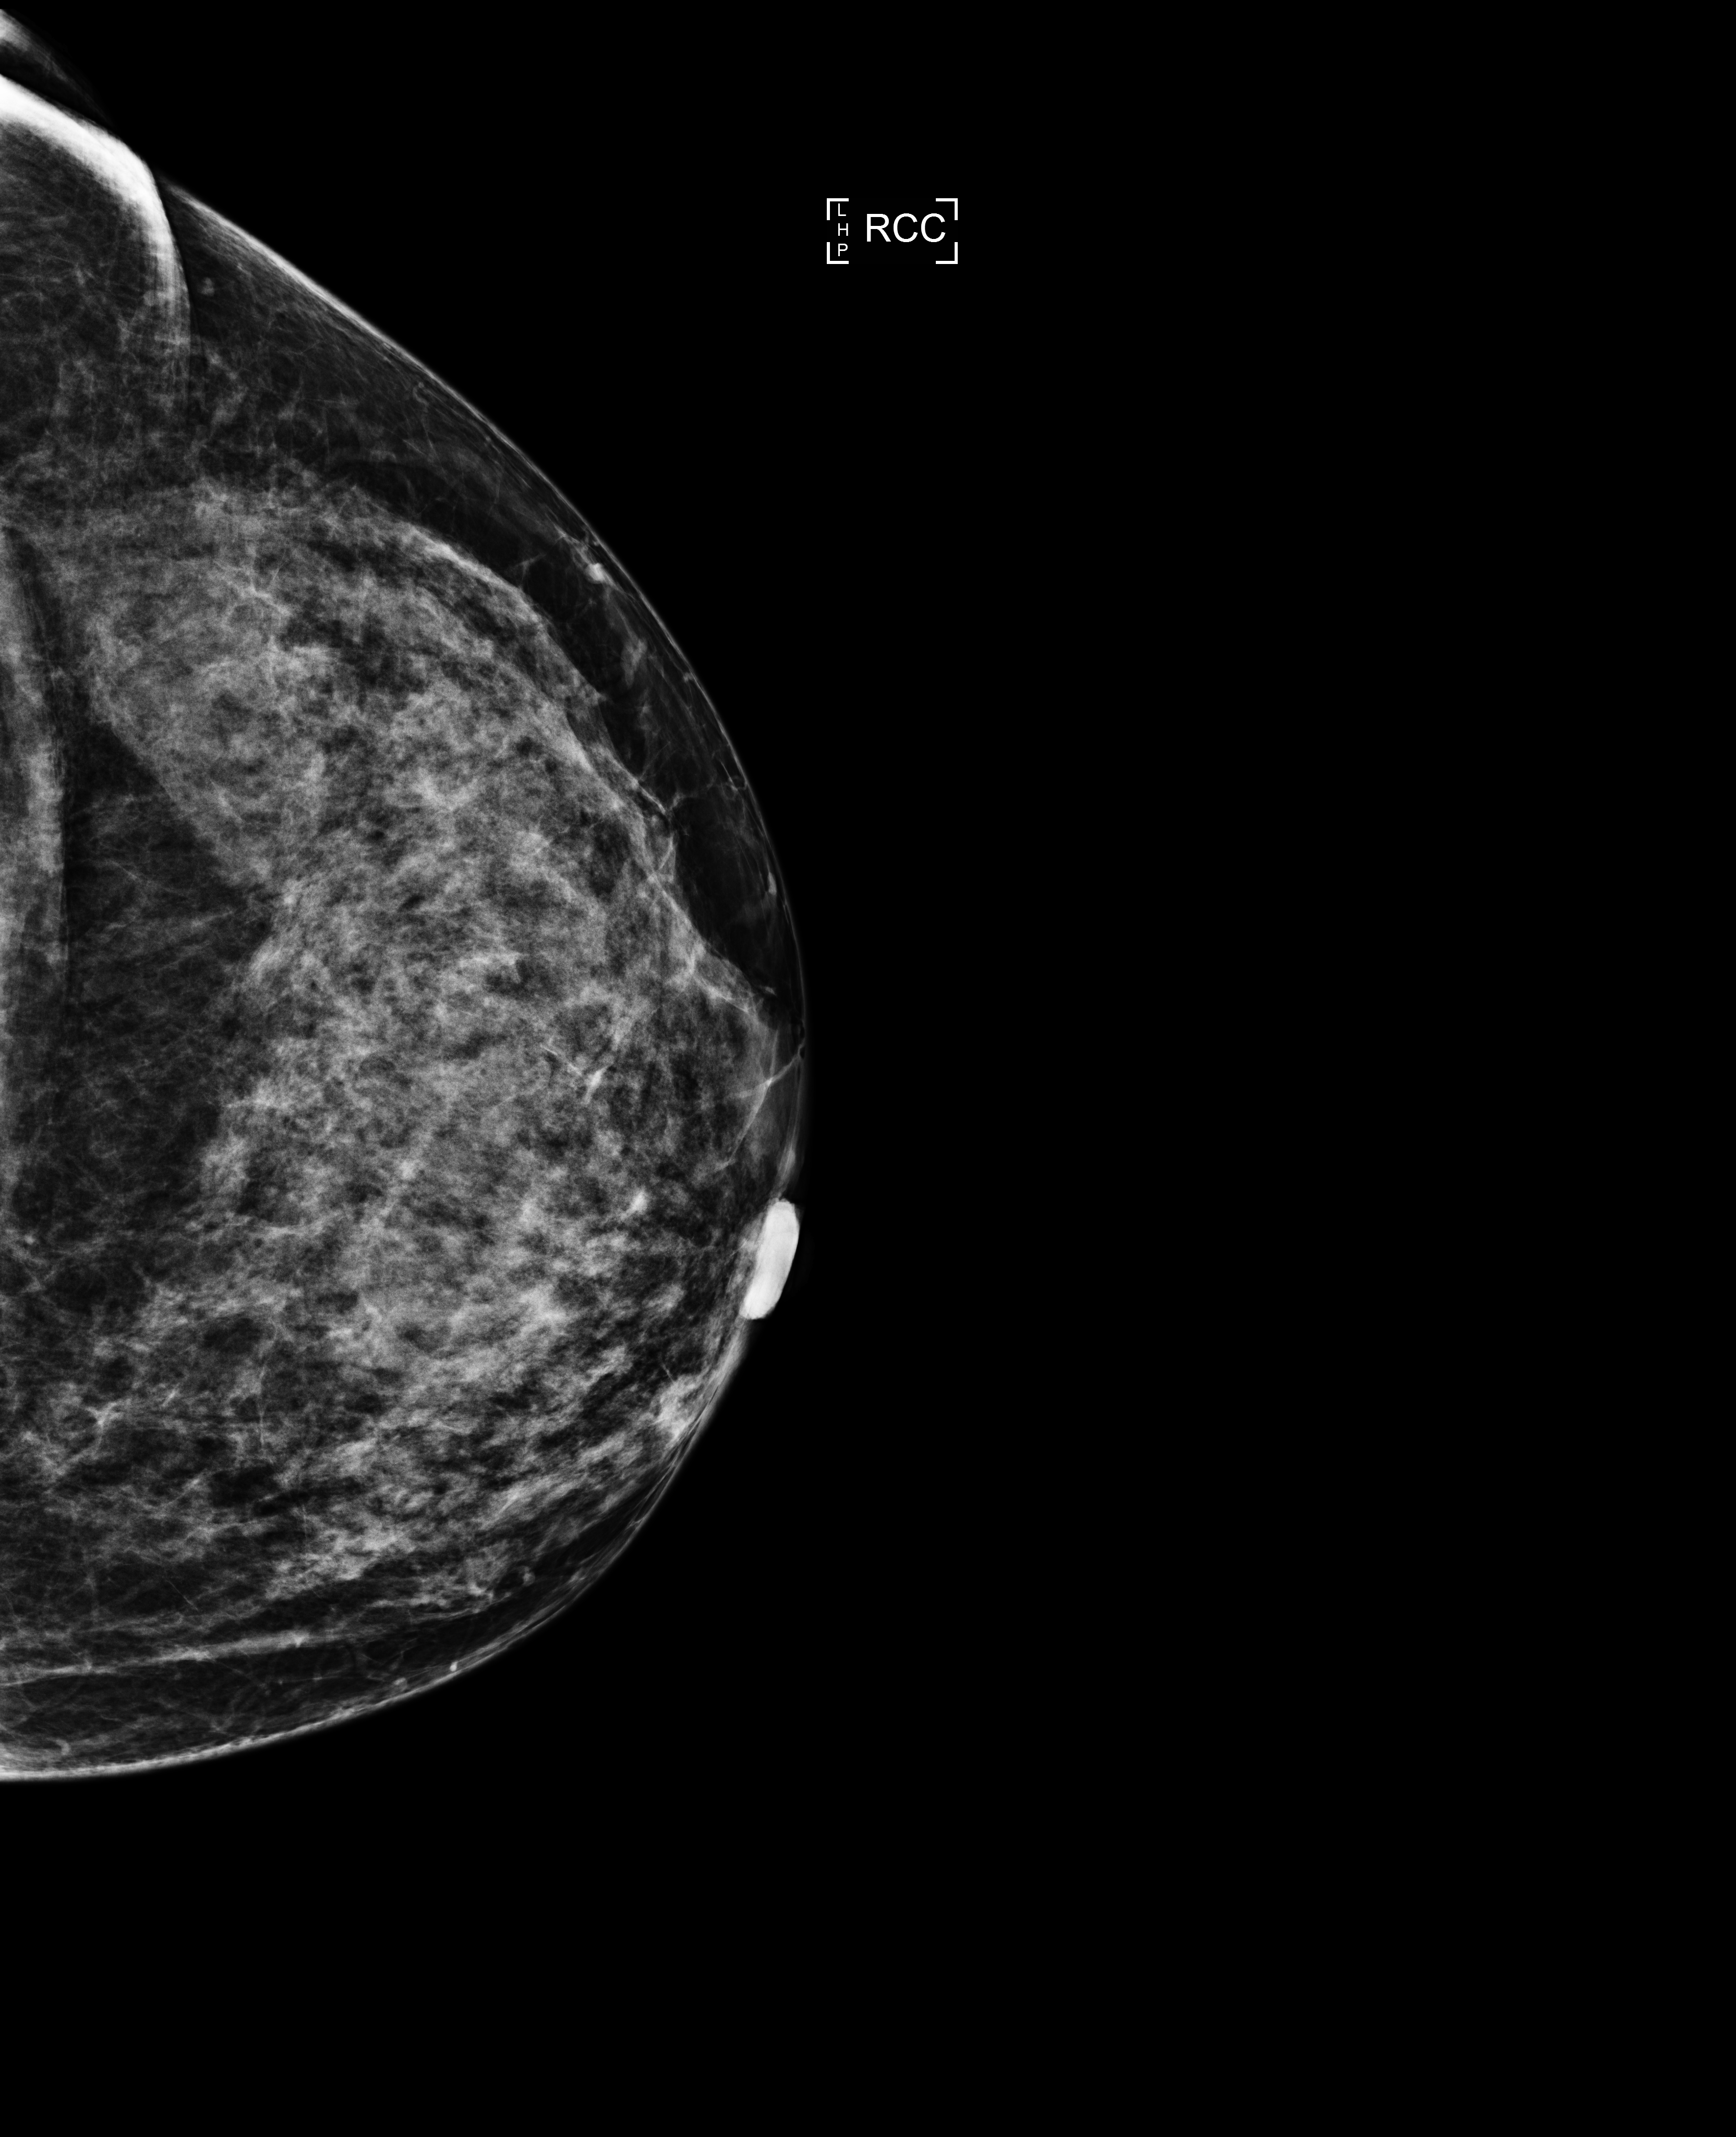
Full-field digital mammogram (FFDM); right breast; CC view; annual screening mammography examination; system: Selenia Dimensions. Patient: female, 42 years.
- BI-RADS breast density category at the screening exam (both breasts, scale 1–4): 3
- final BI-RADS assessment for this screening round (tomosynthesis exam, both breasts): category 1
- recall: no recall after this screen